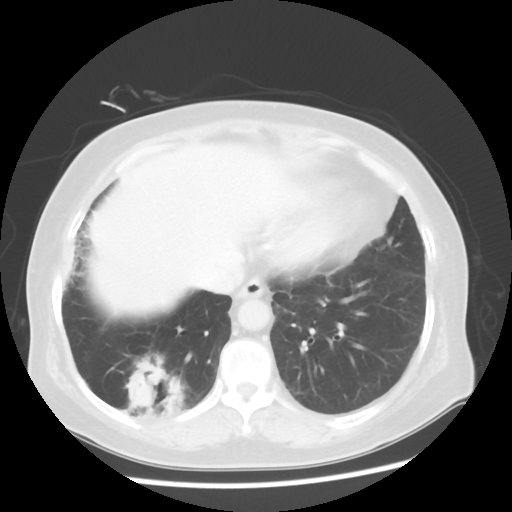
Chest CT, one axial slice. Slice 16 of 56 in the series (ordered by position). Reconstruction kernel STANDARD. 120 kVp. Lung window (W 1500 / L -600 HU). 512 × 512 image matrix. Female patient, age 64 years. From the clinical record (not read from this slice): clinical TNM (as recorded): Tis N0 M0.
Structures marked on this image (rectangle marked by the reading radiologist):
- lung tumour (recorded histology: adenocarcinoma): bounding box (x1, y1, x2, y2) in pixels: (117, 346, 200, 437)